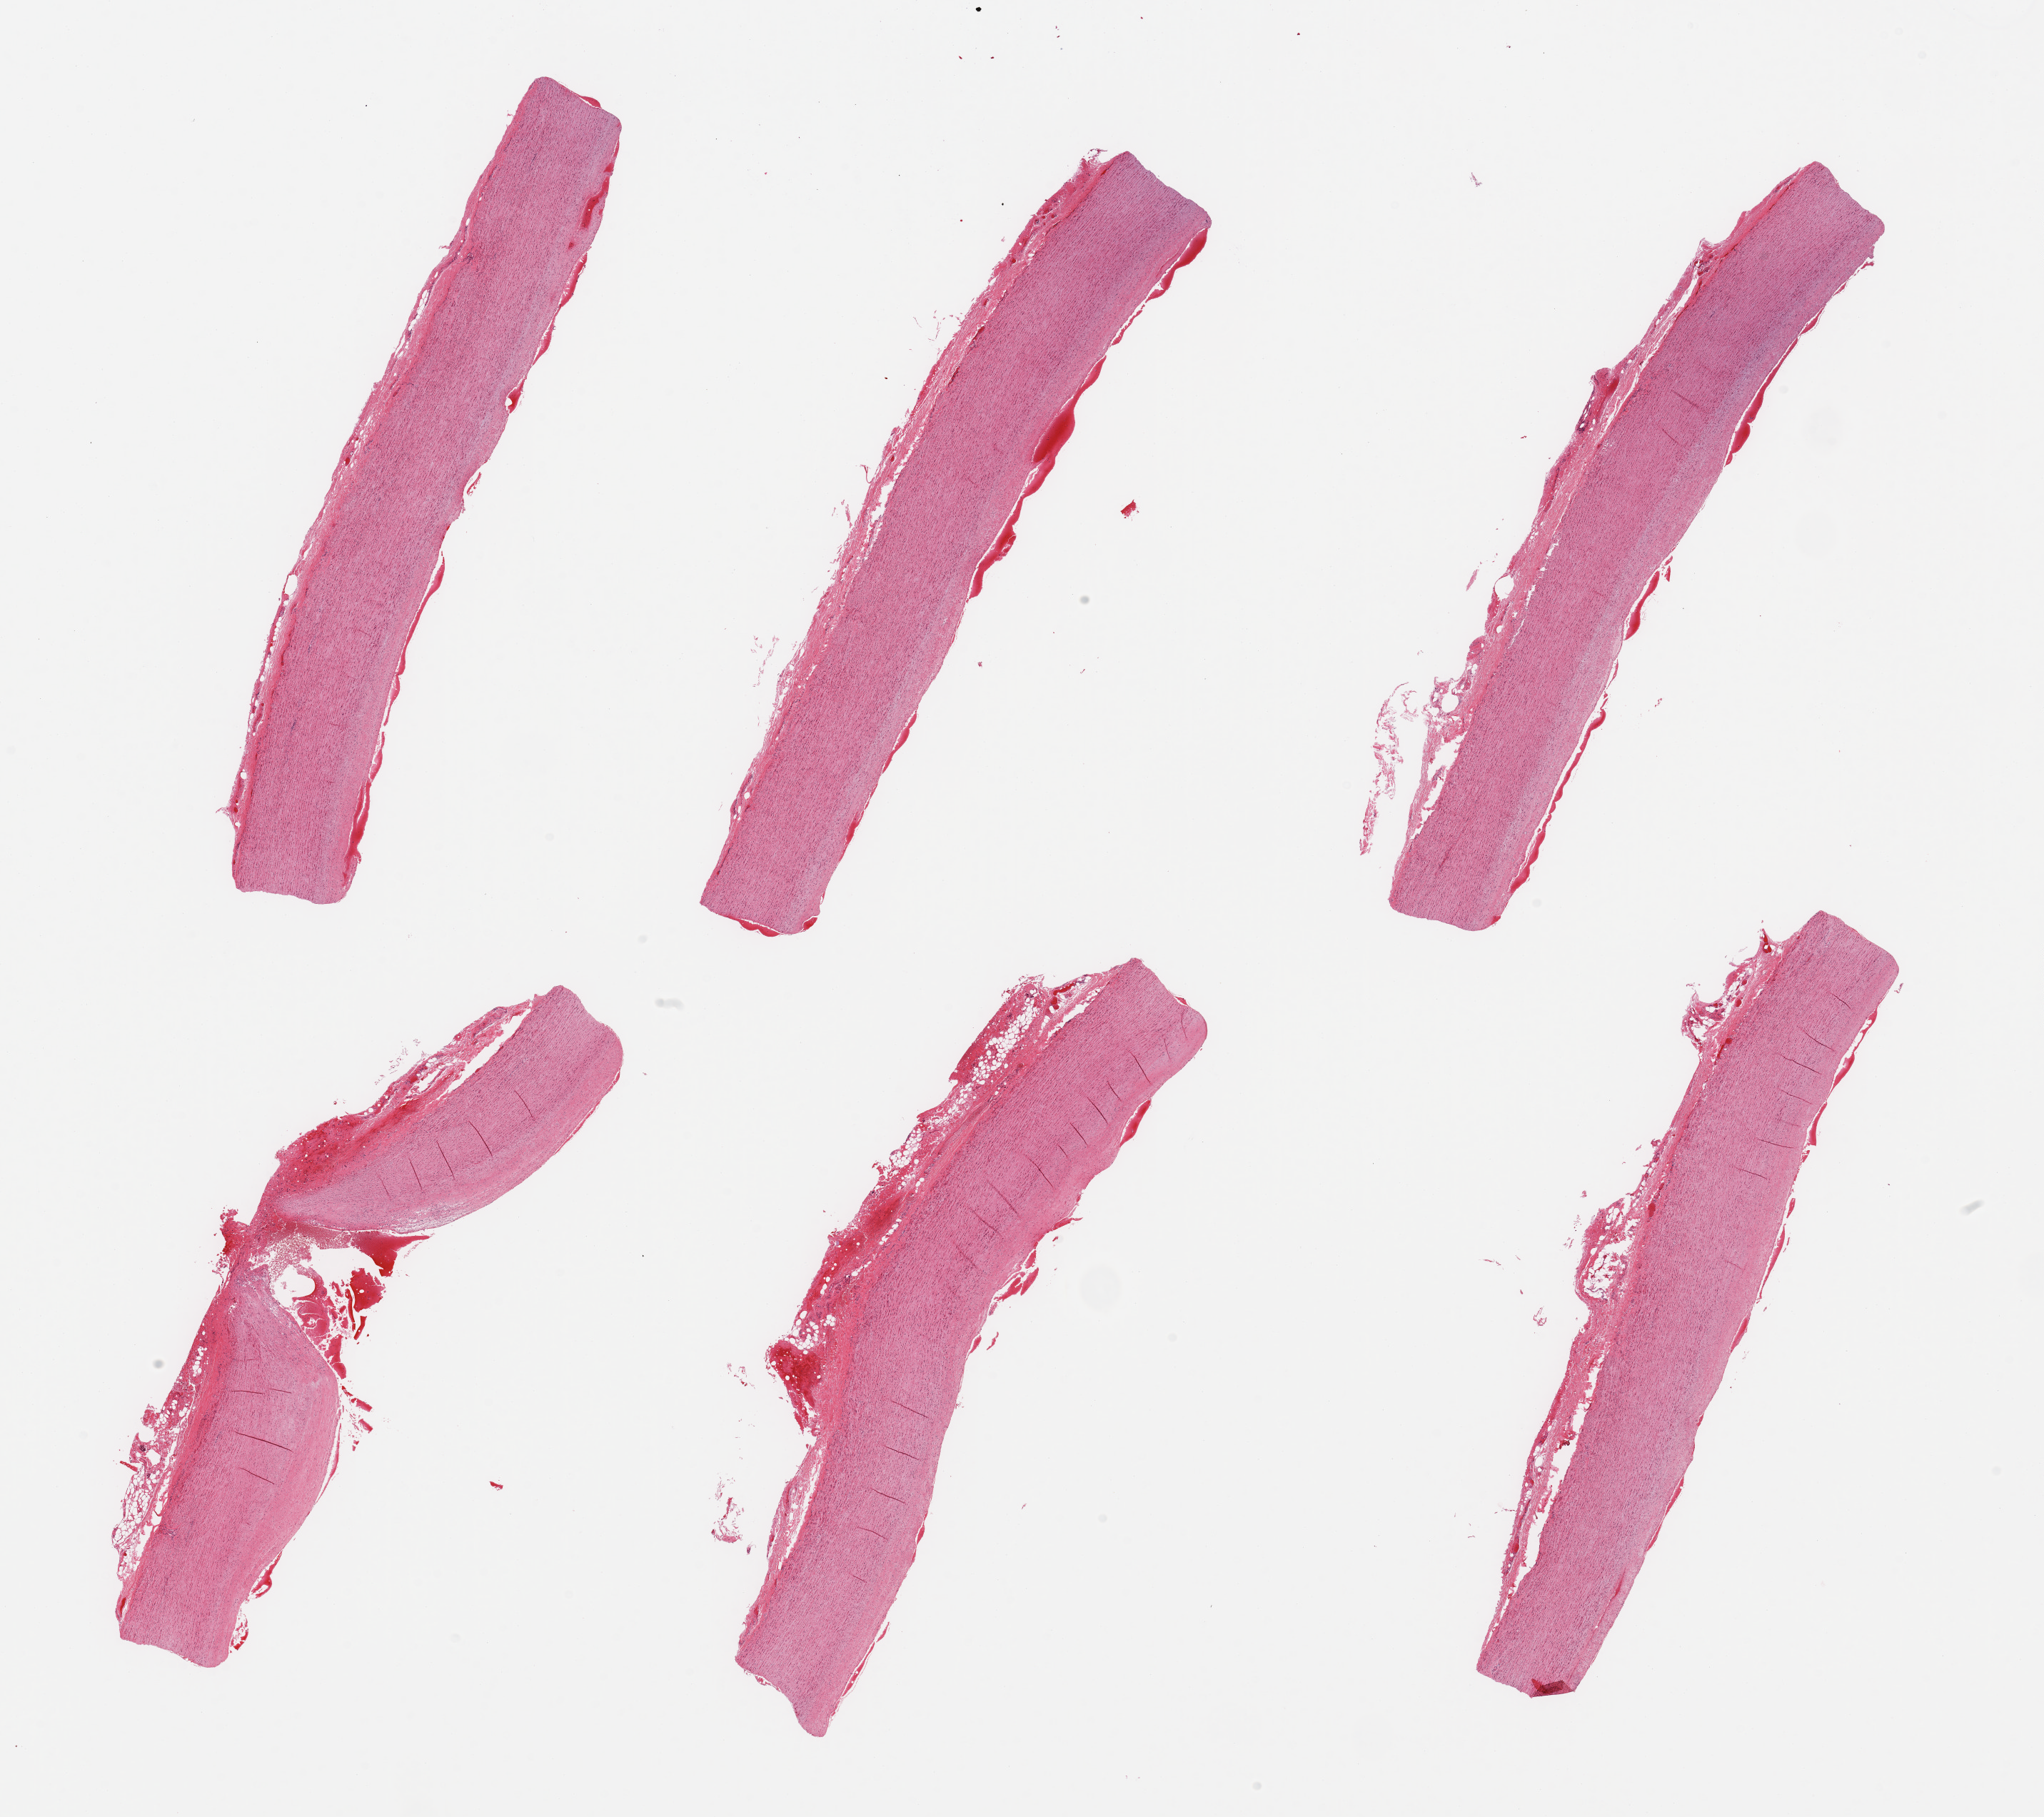
Whole-slide image, H&E stain — low-resolution overview of the scanned area, about 22.6 x 20.1 mm (acquisition: 20x scan); PAXgene-fixed, paraffin-embedded tissue; target tissue: aorta; tissue donor sample.
- pathologist's review note for this sample: 6 pieces; fibrosclerotic plaque , ~0.9 mm attached adventitia